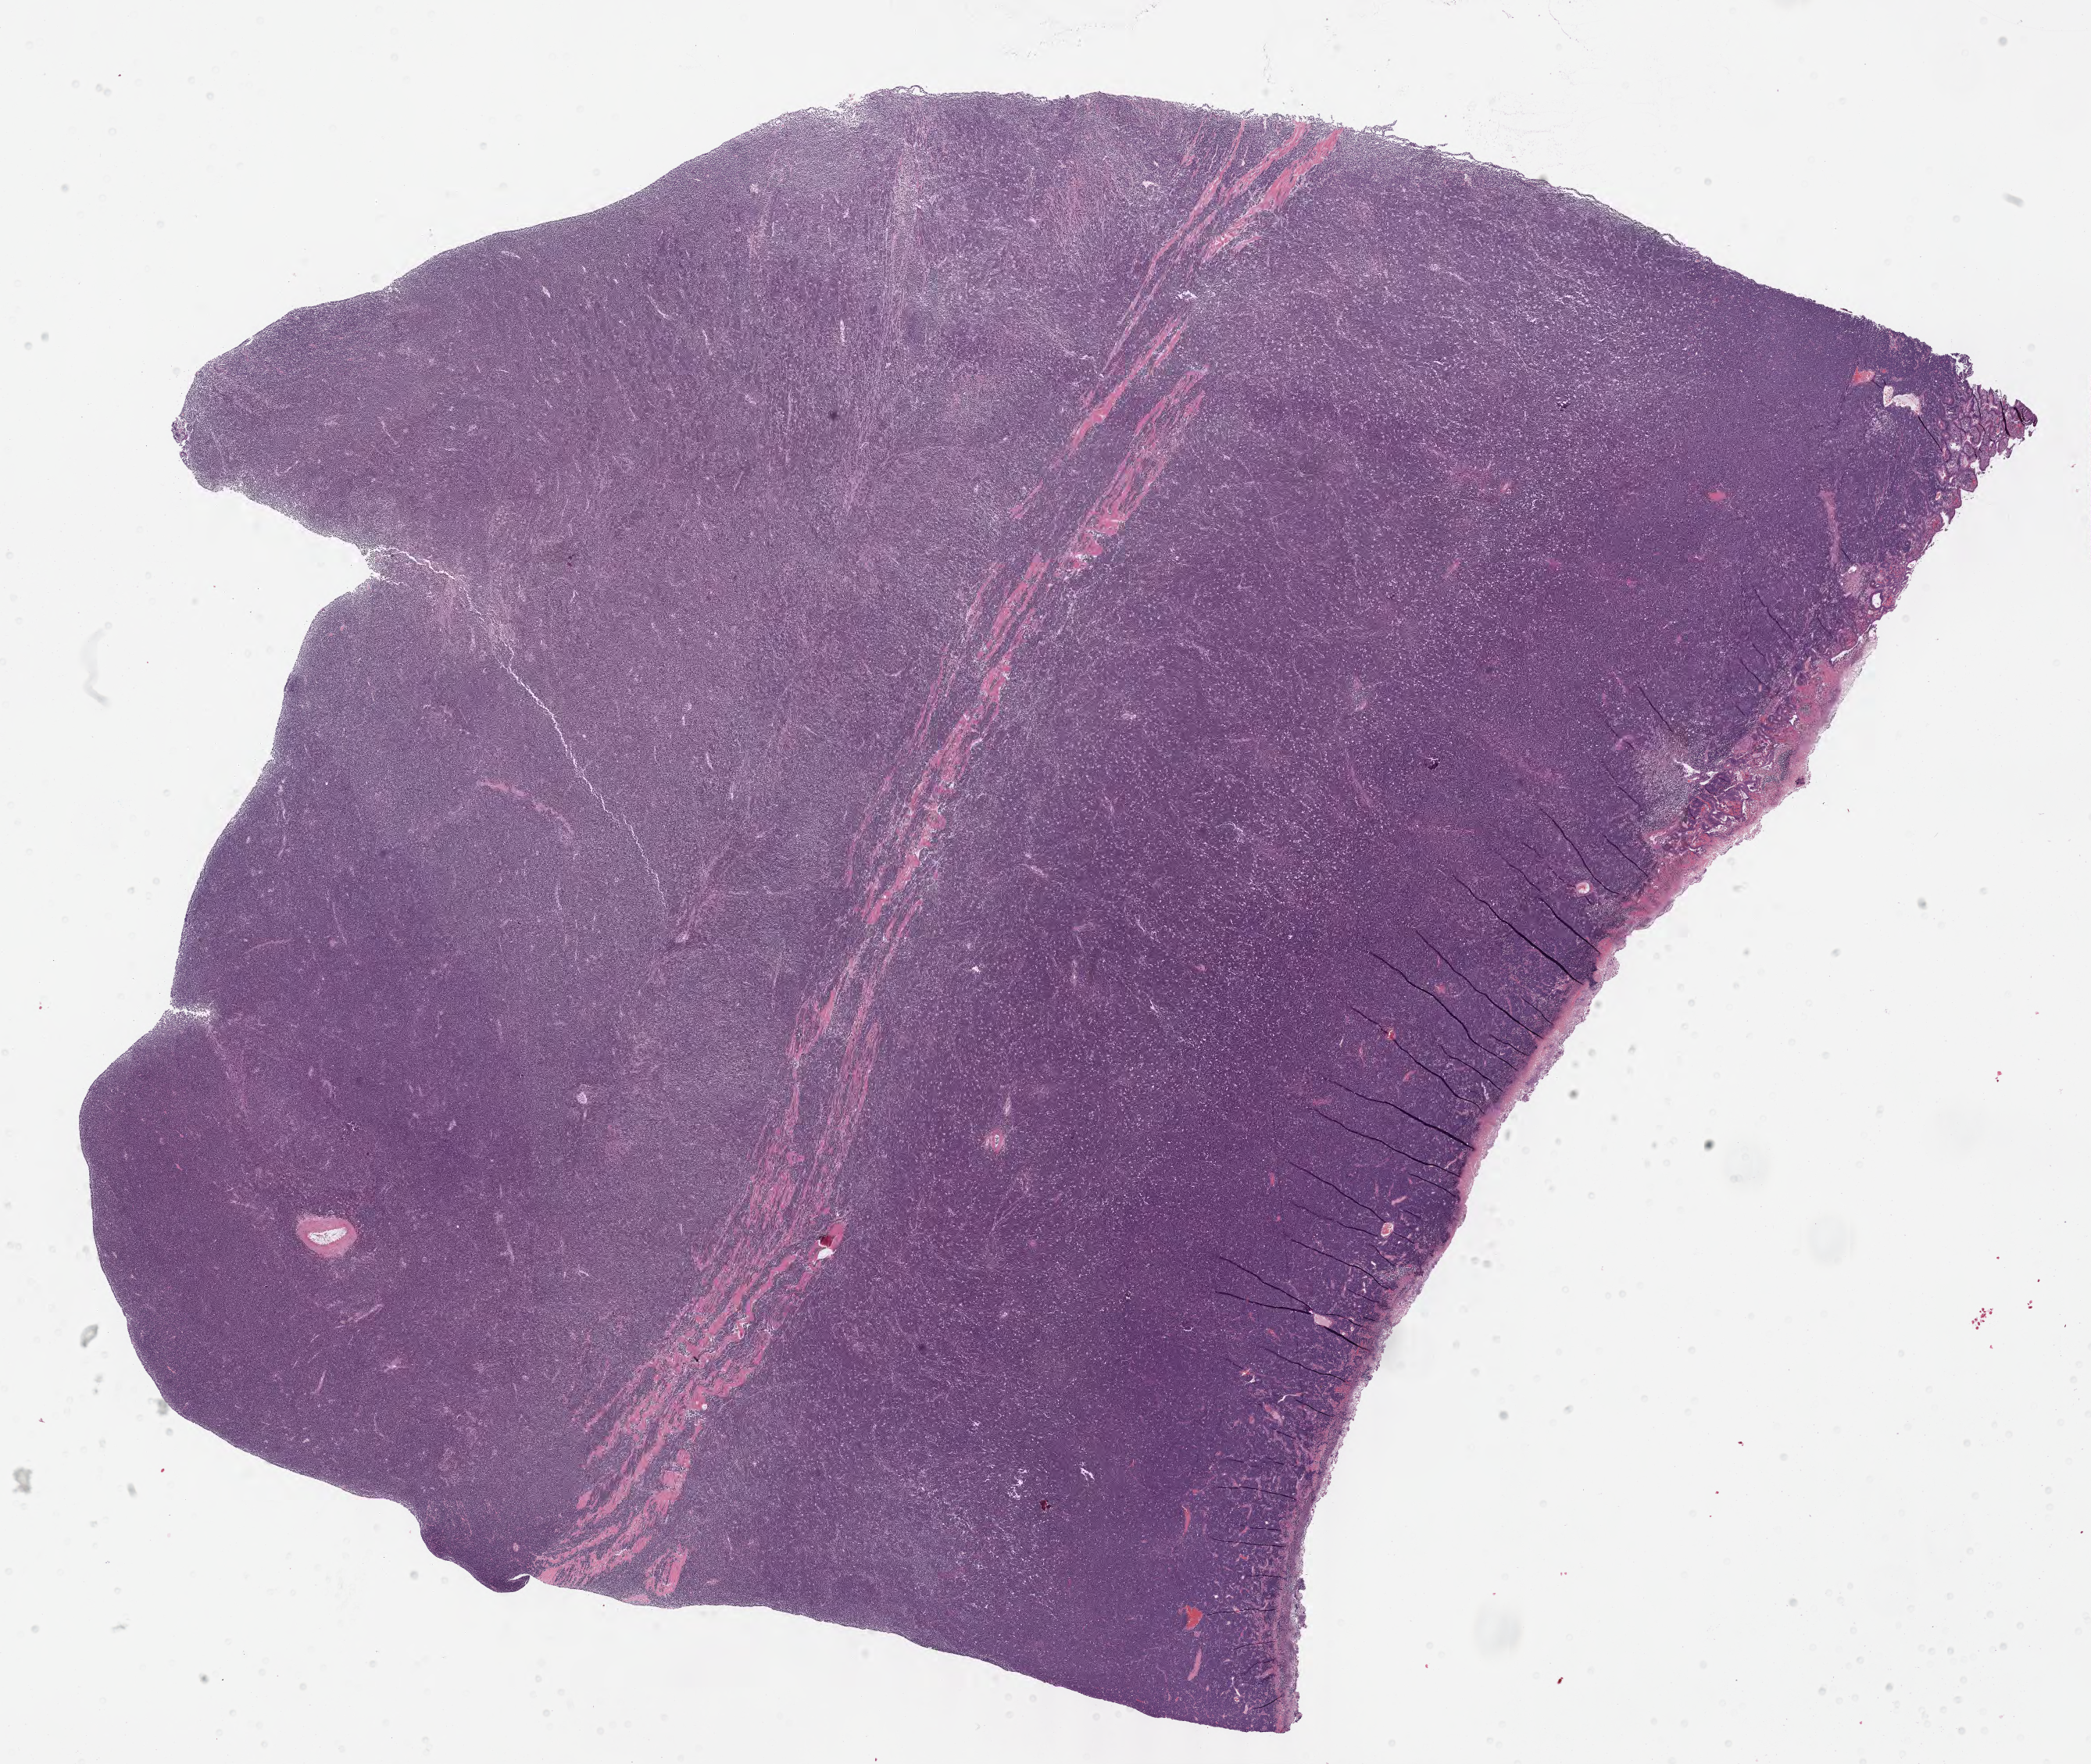
Whole-slide image, H&E stain — whole scanned area (about 21.6 x 18.2 mm) shown as a low-resolution overview; specimen: tumor tissue. Male patient, aged 36.
Diagnosis: Burkitt lymphoma, NOS.